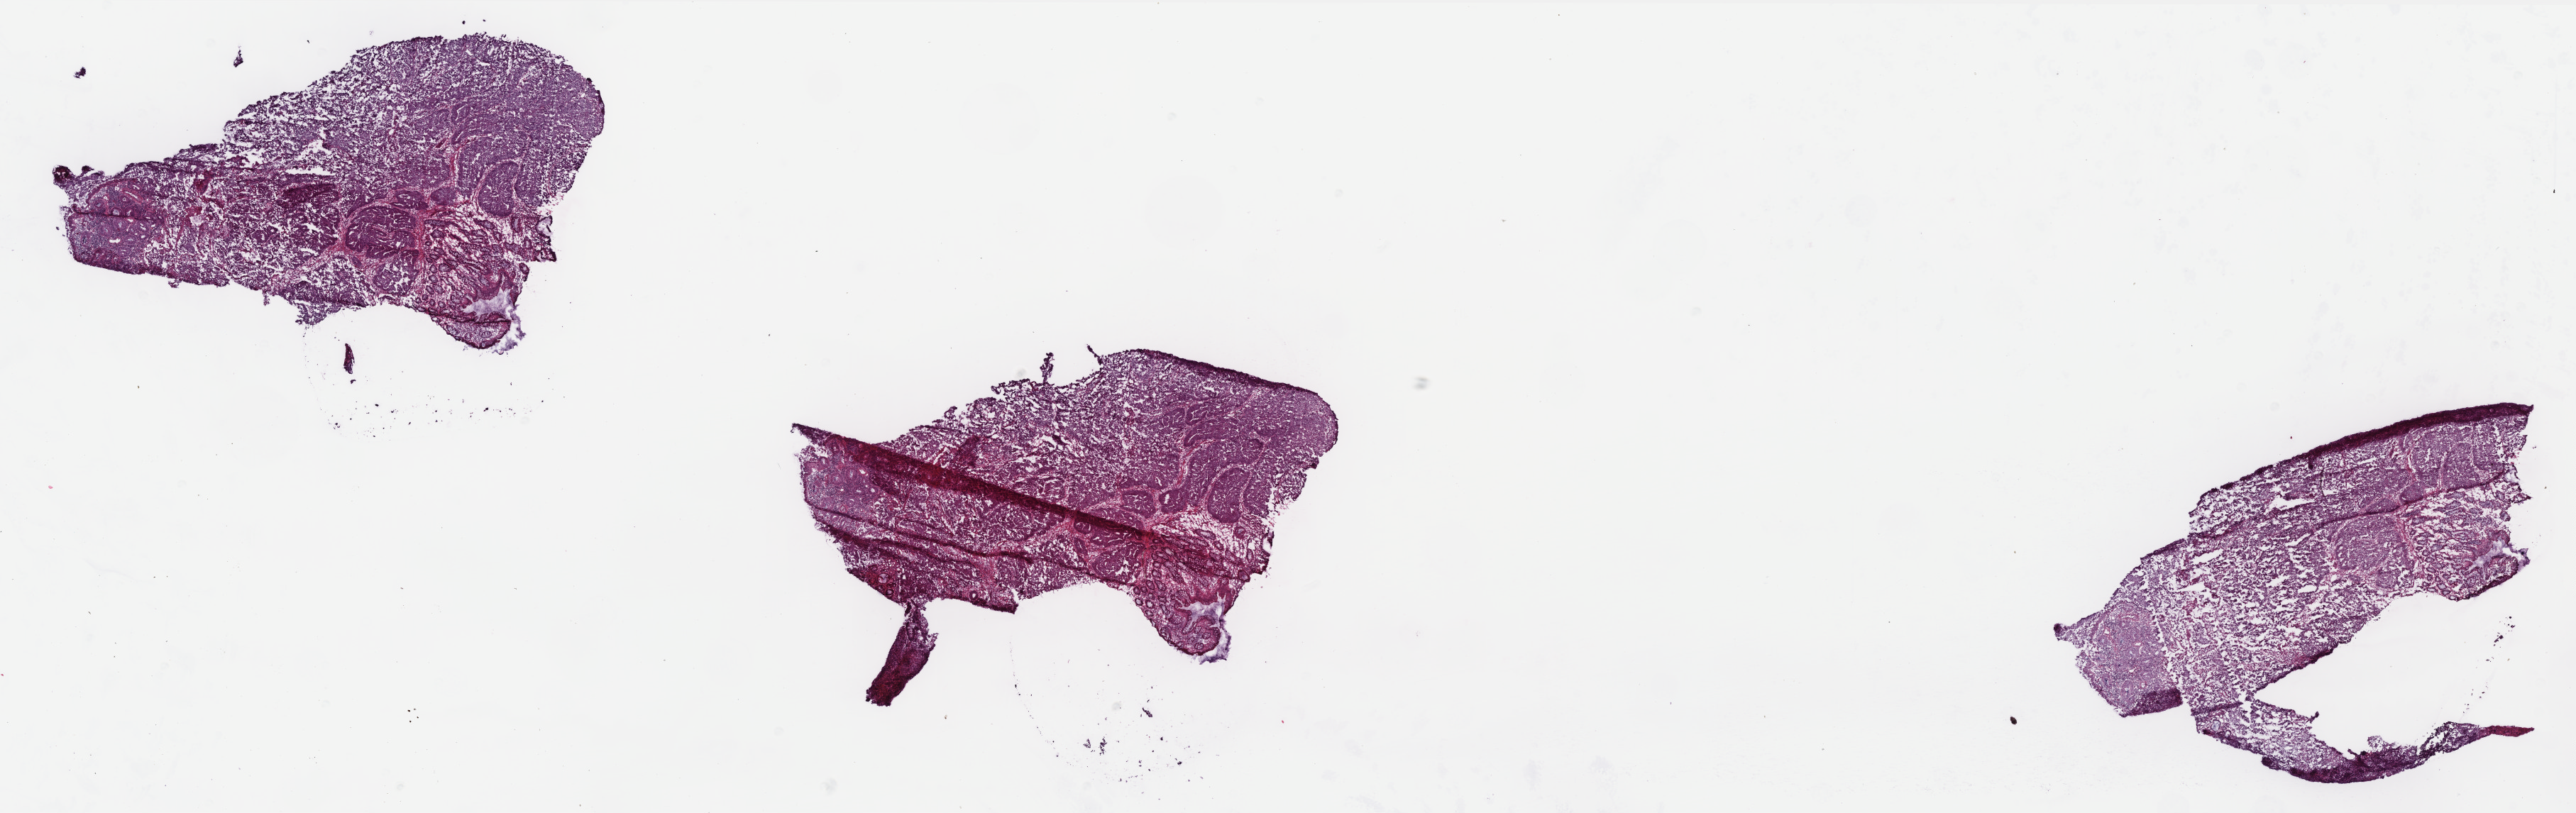
H&E-stained whole-slide image — a low-resolution overview of the entire scanned area, about 29.1 x 9.2 mm (from a 40x scan), frozen section from the top of the tissue portion, primary tumour sample from the rectum. Female, age 62 years at initial diagnosis.
Diagnosis: Adenocarcinoma, NOS.